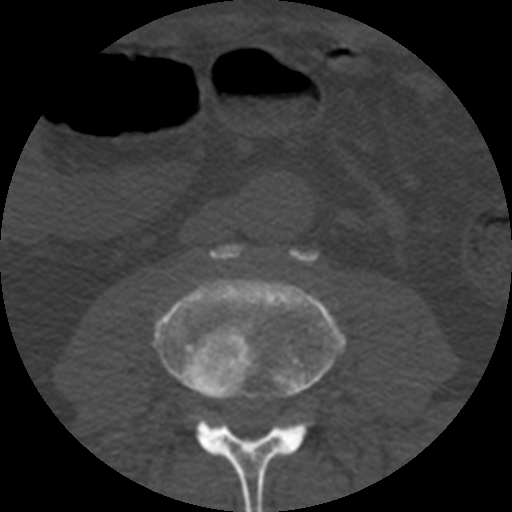
CT including the spine, one axial slice. Reconstruction kernel STANDARD. Bone window (W 1800 / L 400 HU). 1.25 mm slice thickness. 512 × 512 image matrix, field of view 160 × 160 mm. Patient age 57 years. From the clinical record (not read from this slice): primary cancer: prostate.
Annotated regions visible in this slice (semi-automatically segmented with operator editing):
- L3 vertebra: bounding box [x1, y1, x2, y2] px = [154, 278, 344, 512]
- L4 vertebra: [213, 245, 318, 263]